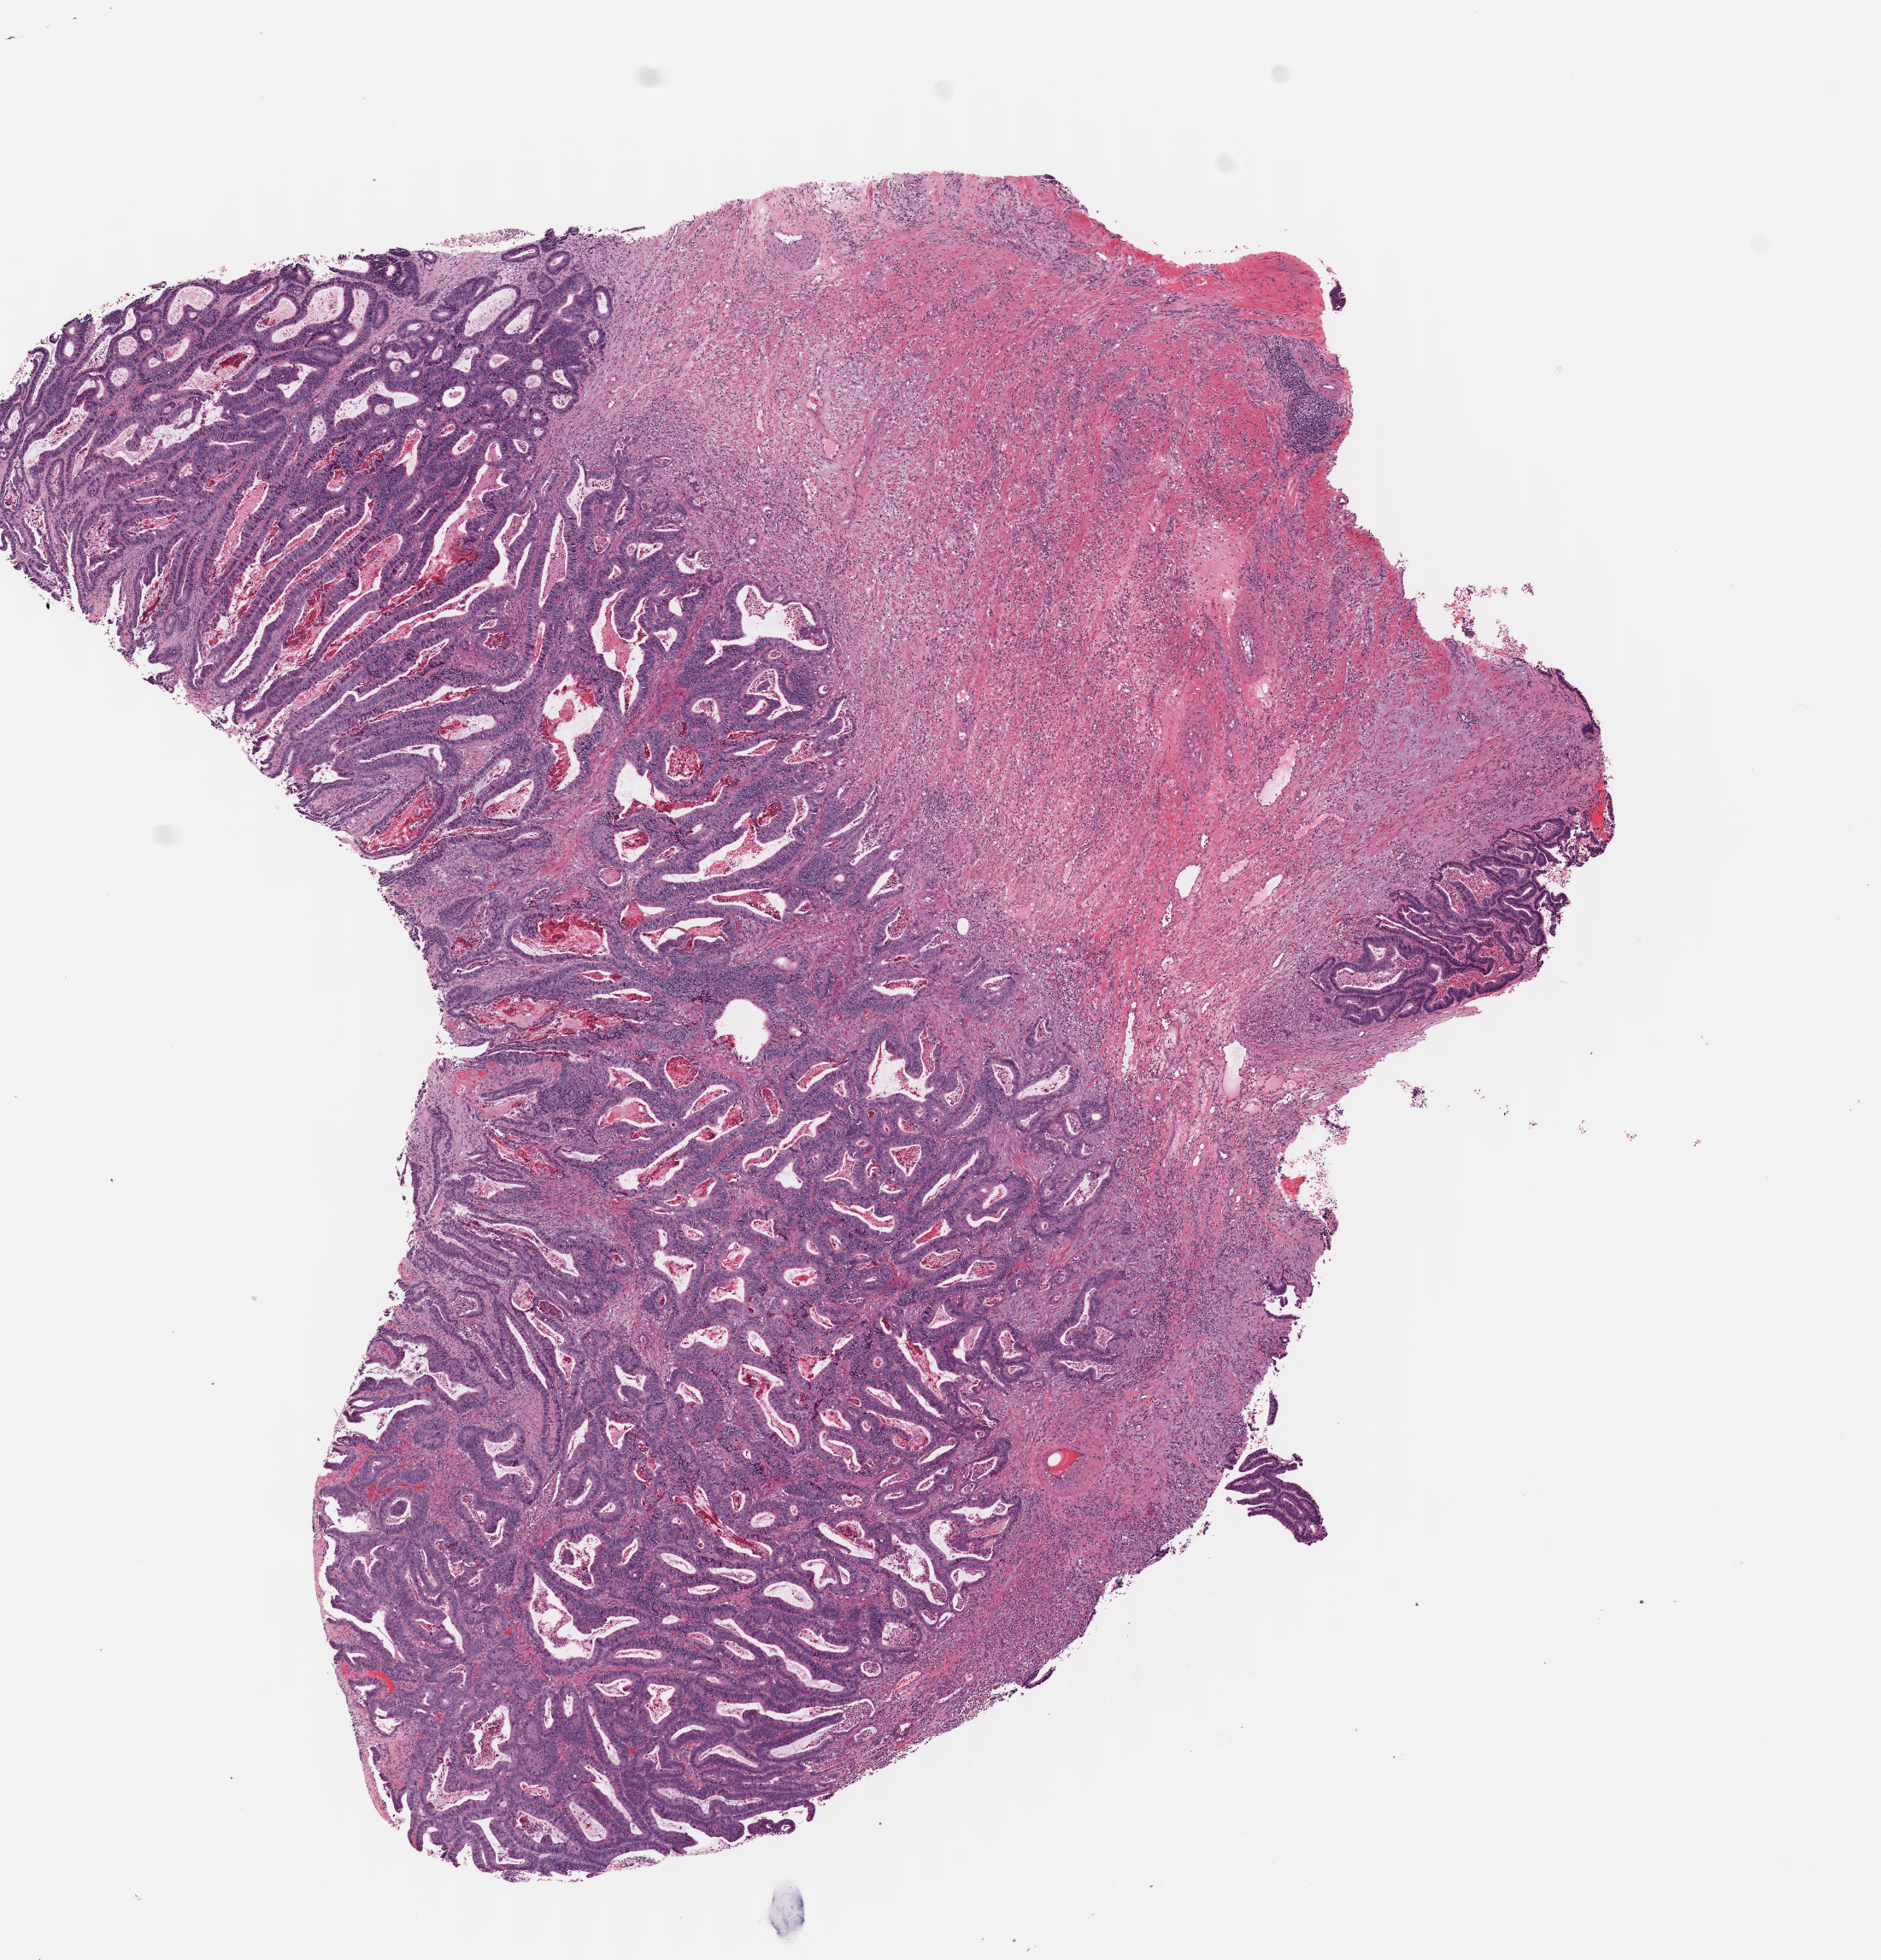
Digitized H&E tissue section (whole slide), shown as a low-resolution overview of the whole scanned area (about 8.7 x 9.0 mm). Frozen section. Sample: primary tumour, colon. Male, age 62 years at initial diagnosis. Slide review estimates, as recorded: tumour cells 30%, tumour nuclei 65%, normal cells 0%, stromal cells 55%, necrosis 15%. Infiltration values recorded for this section: lymphocyte infiltration 10%, monocyte infiltration 3%, neutrophil infiltration 10%.
Lymph nodes positive (case pathology): 0 of 30 examined. Diagnosis: Adenocarcinoma, NOS. AJCC pathologic stage: IIA.